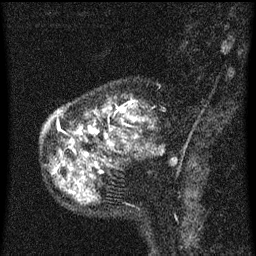
Breast MRI (dynamic contrast-enhanced), one sagittal slice; position 18 of 60 along the scan axis; dynamic contrast-enhanced series, image 2 of 3 at this slice position (ordered by acquisition); 1.5 T; TE 4.2 ms, TR 8 ms; 2 mm slice thickness; 256 × 256 image matrix. Female patient, age 55 years.
Structures marked on this image (semi-automatic segmentation, software-assisted and operator-edited):
- analysis volume of interest (the breast-tissue region the enhancement analysis was run in; not a lesion): bounding box [x1, y1, x2, y2] px = [42, 80, 166, 155]
- tumour enhancement mask (voxels above the 70 % enhancement threshold inside the analysis volume of interest): [57, 102, 145, 147]